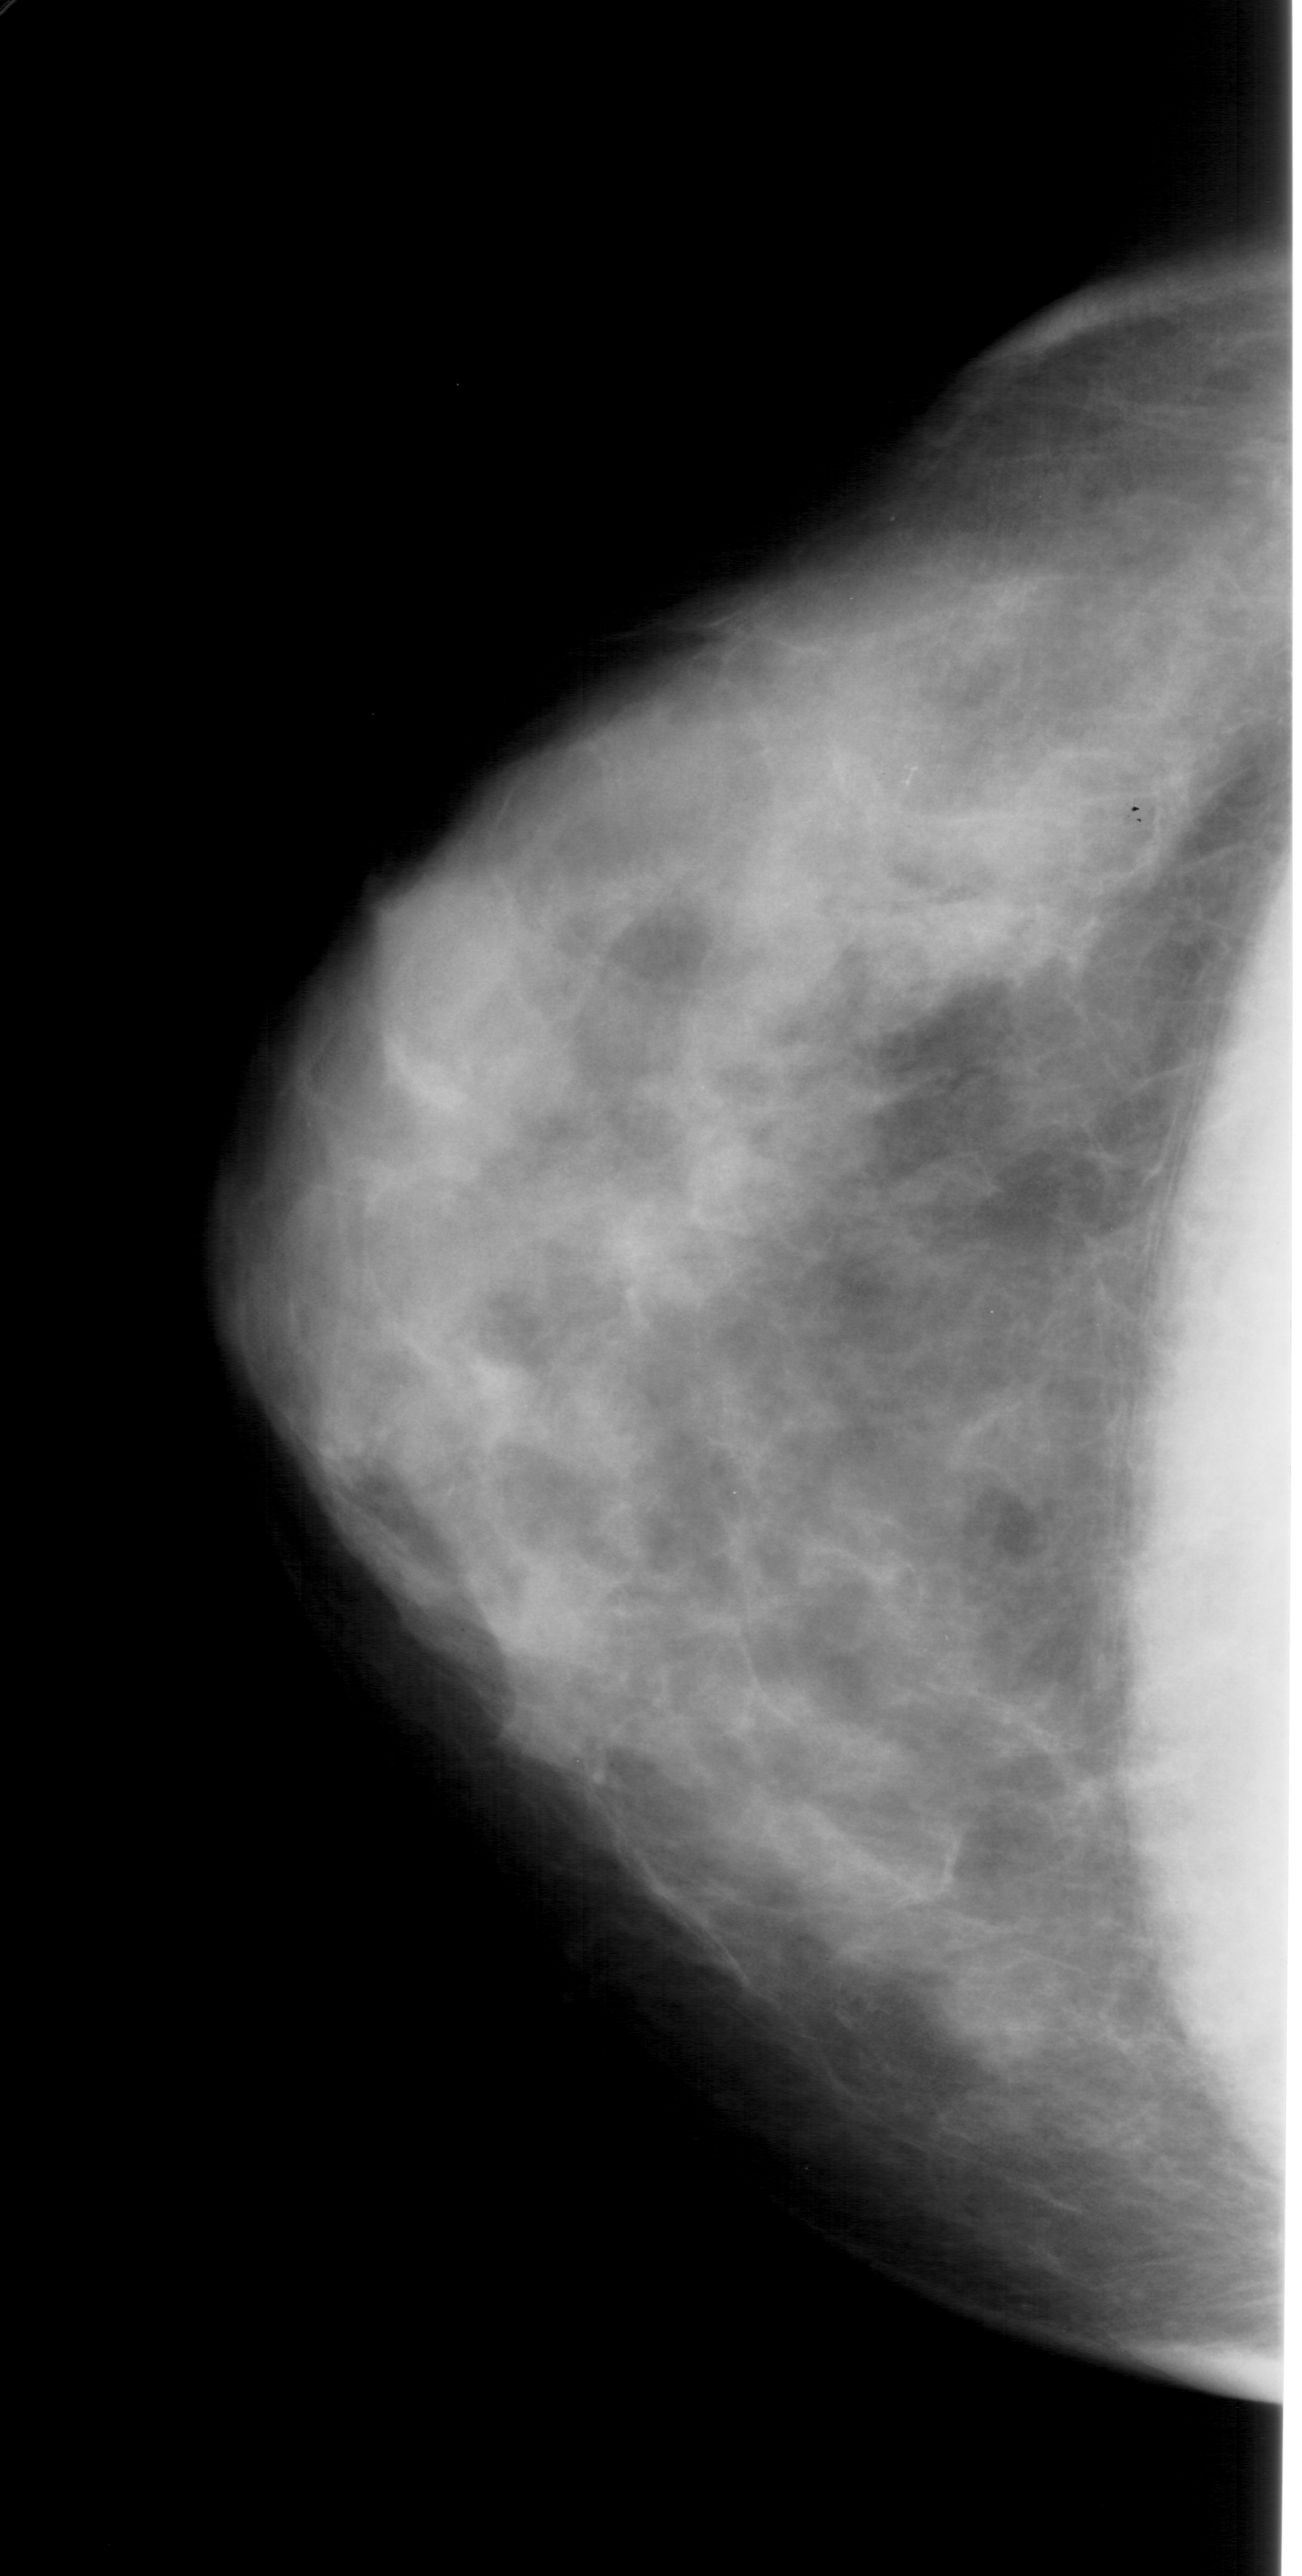
Mammogram (digitized film). Left breast. Craniocaudal (CC) view. 1302 × 2576 image matrix.
Expert-marked regions of interest on this image (one box per marked abnormality):
- calcifications, morphology pleomorphic, distribution clustered; BI-RADS assessment category 4; pathology result (as recorded, not read from the image): benign: bounding box [x1, y1, x2, y2] px = [869, 729, 967, 807]